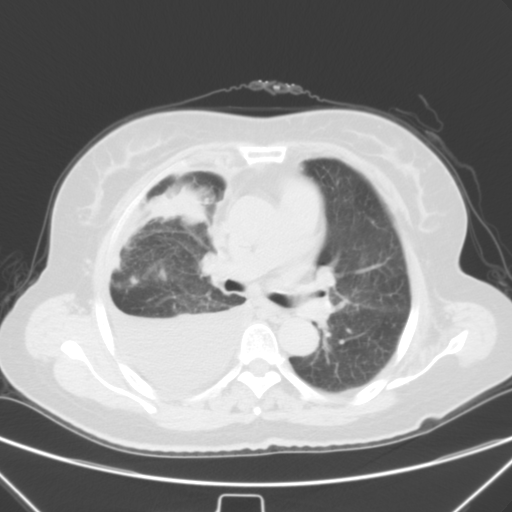
Chest CT, one axial slice. 120 kVp. Lung window (W 1500 / L -600 HU). 5 mm slice thickness. 512 × 512 image matrix. Patient: female, 66 years. Case-level facts recorded for this patient, not image findings: clinical TNM (as recorded): T2 N0 M1.
Structures marked on this image (rectangle marked by the reading radiologist):
- lung tumour (recorded histology: adenocarcinoma): bounding box (x1, y1, x2, y2) in pixels: (146, 191, 213, 224)